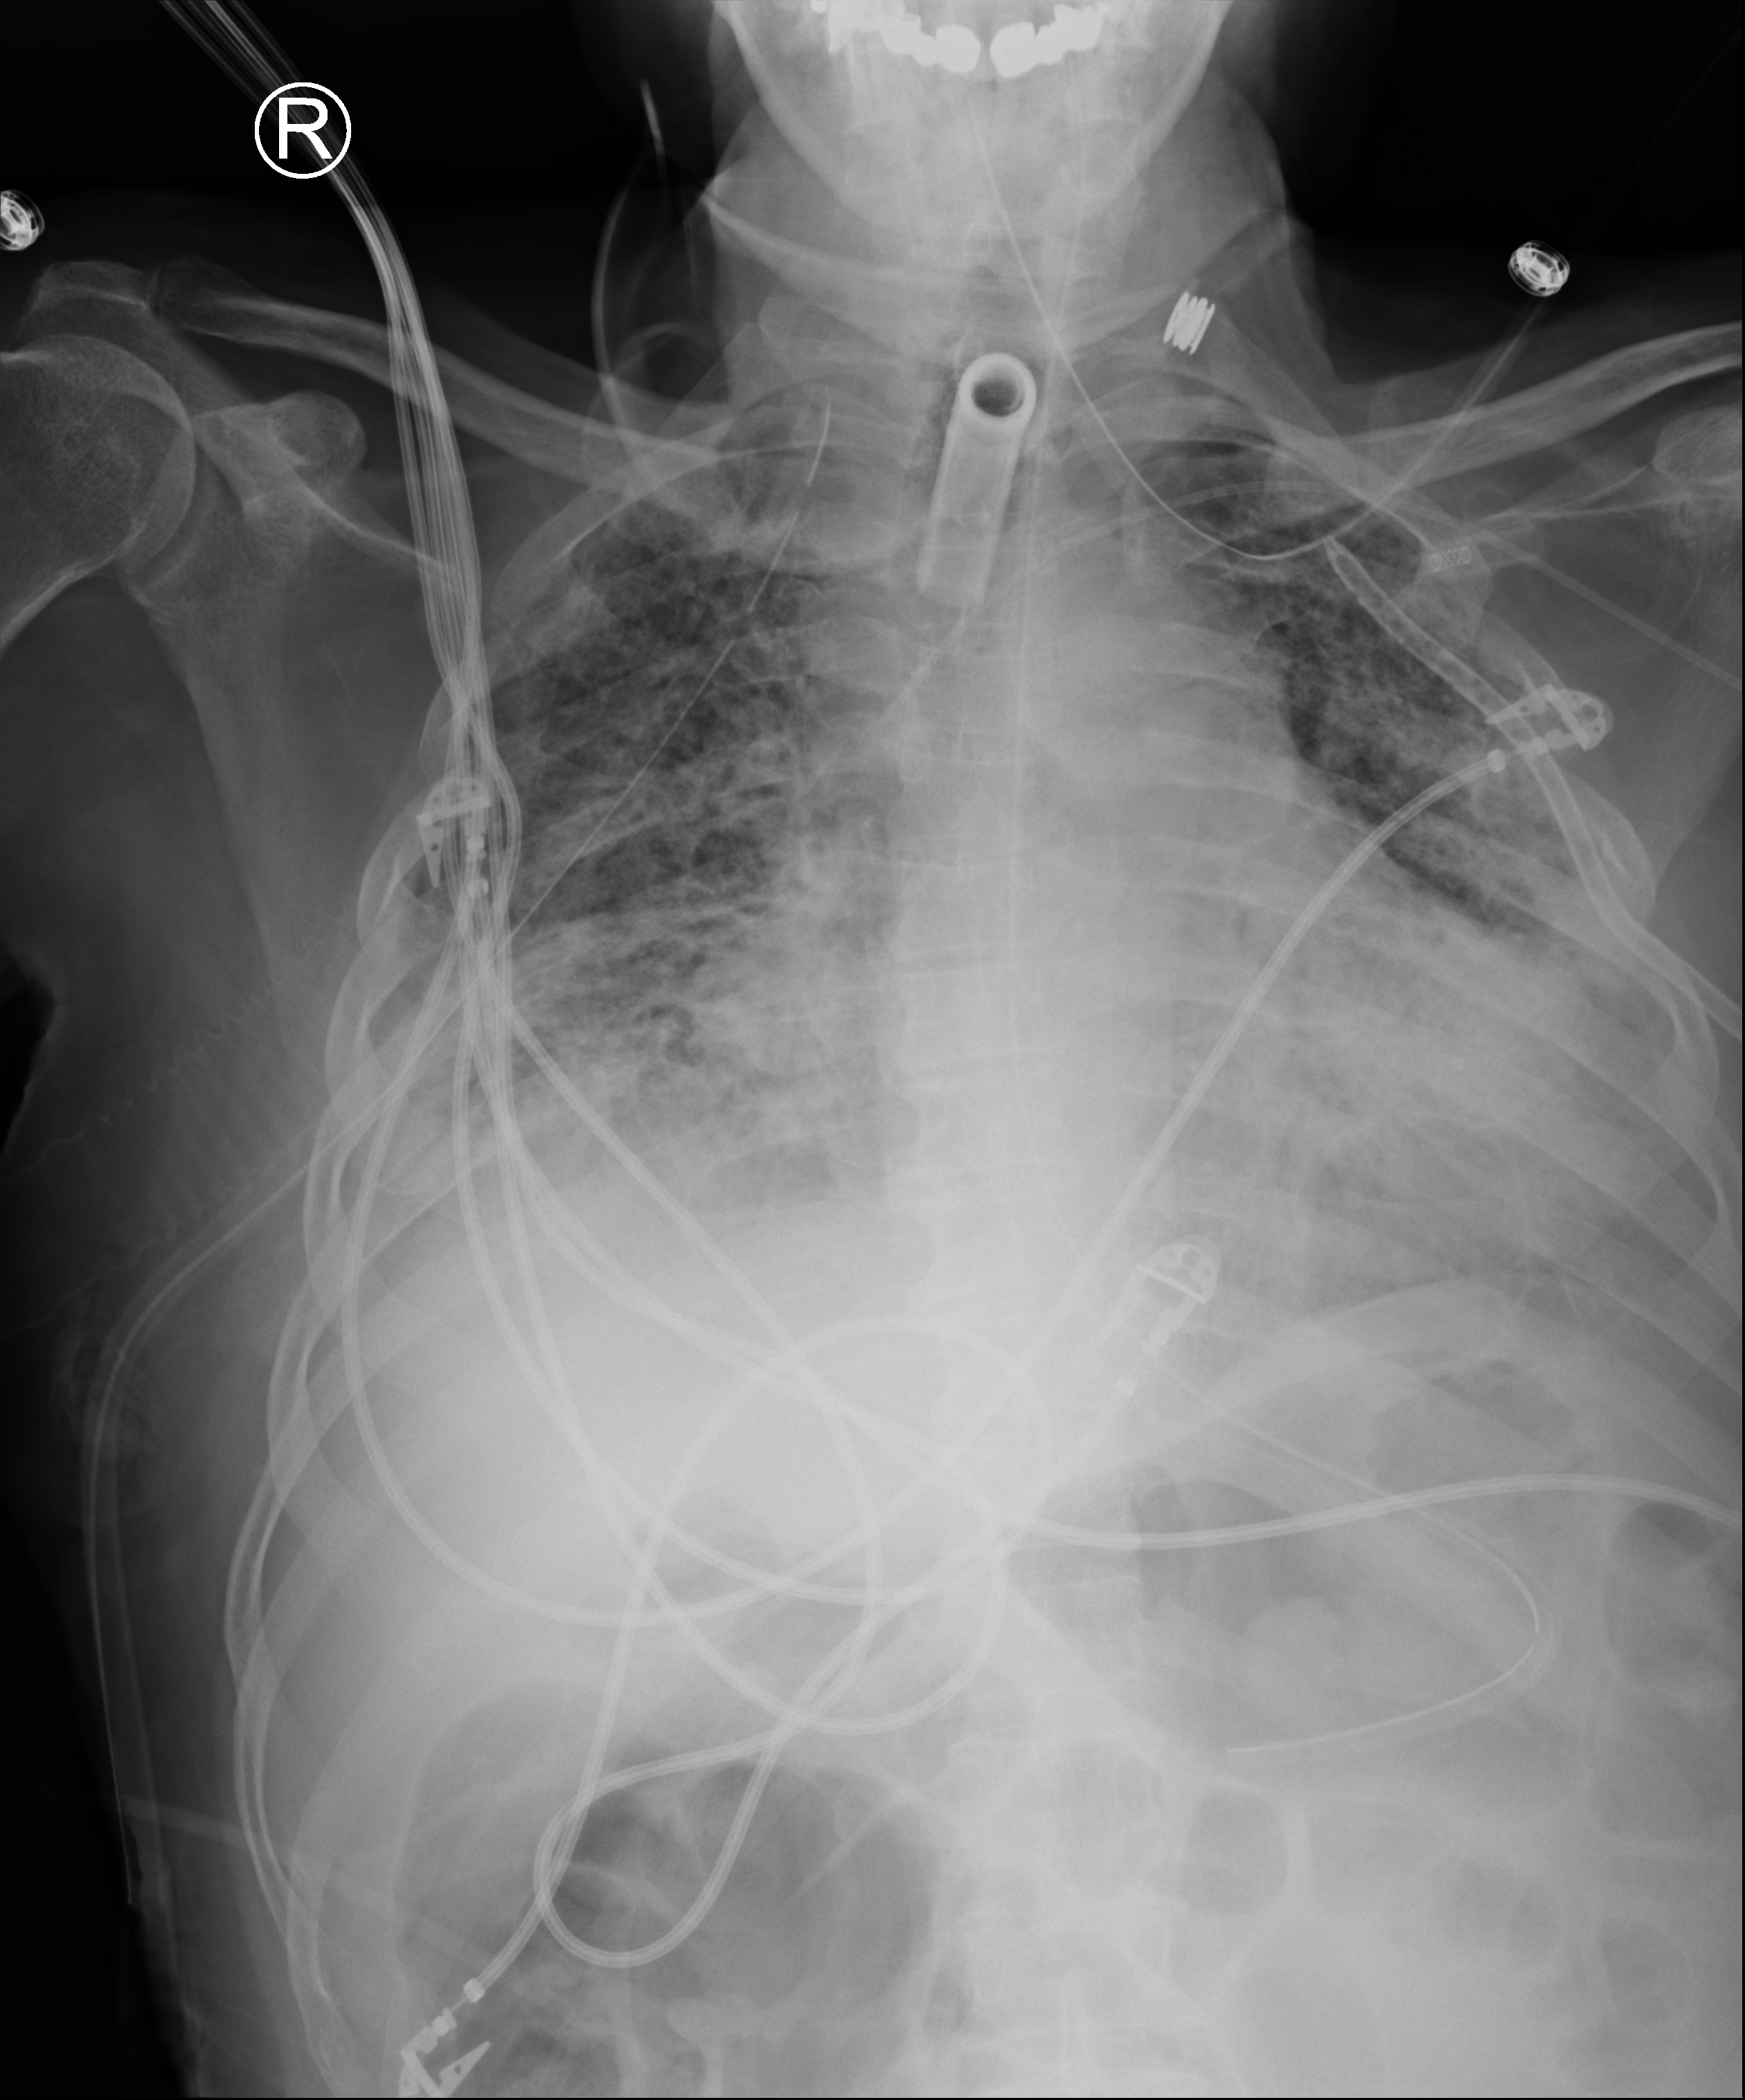
Chest X-ray (portable), anteroposterior (AP) projection. Male patient hospitalised with COVID-19, age 18–59 years.
Admission-level facts for this patient (not findings on this image; timing relative to this image not recorded):
- mechanically ventilated during this hospital stay: yes
- admitted to intensive care during this hospital stay: yes